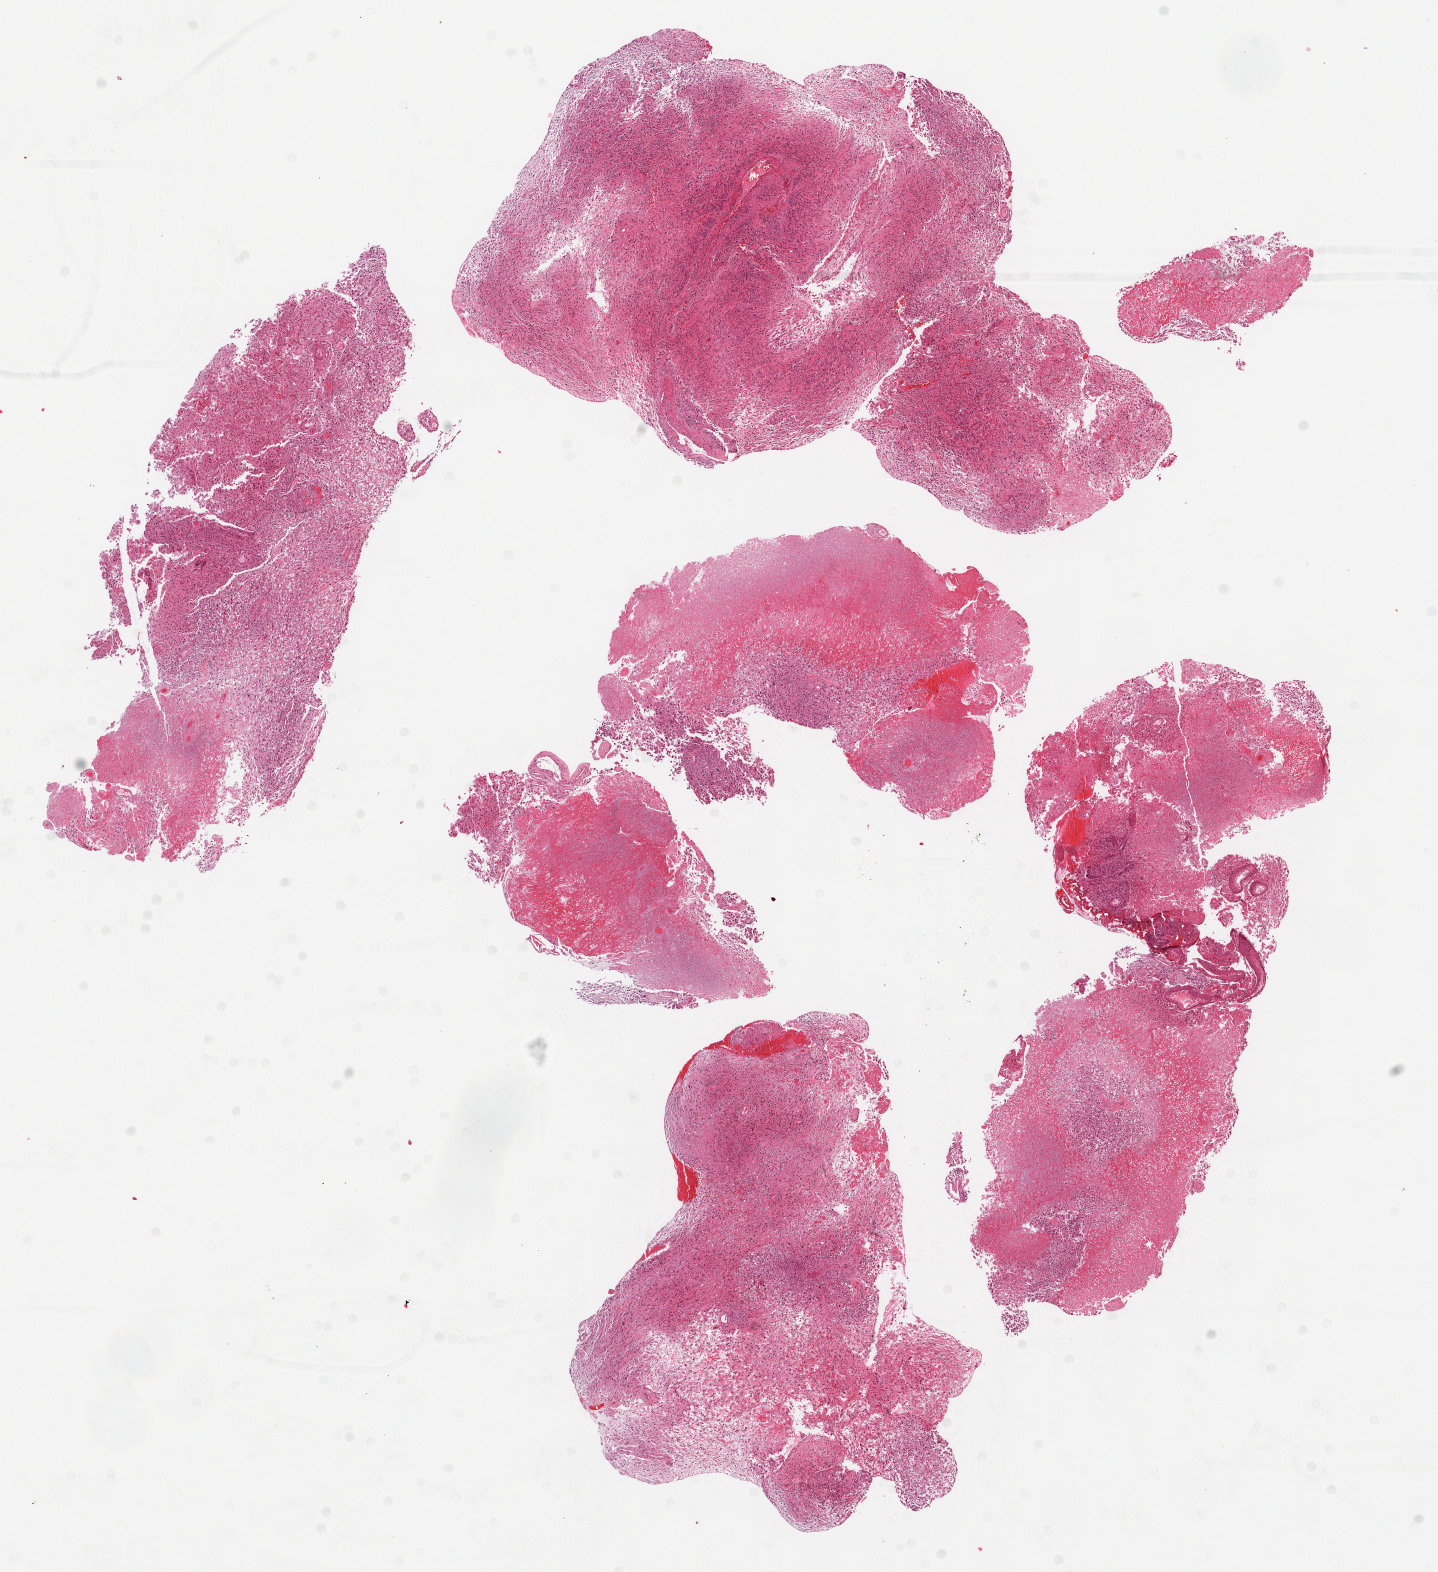
Digitized H&E tissue section (whole slide) — whole scanned area (about 11.6 x 12.7 mm) shown as a low-resolution overview. Formalin-fixed paraffin-embedded (FFPE) diagnostic section. Sample: primary tumour, brain. Male, age 78 years at initial diagnosis.
Diagnosis: Glioblastoma.